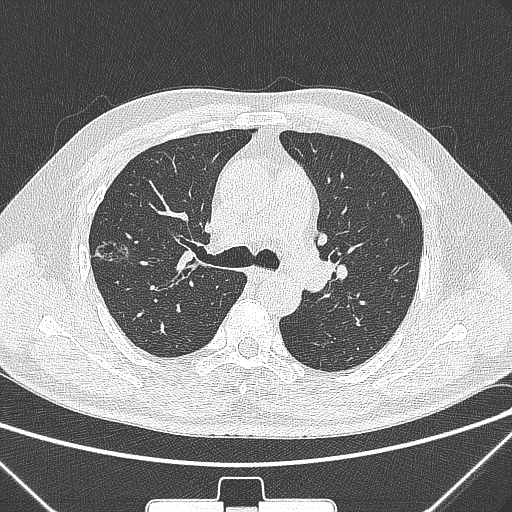
Chest CT, one axial slice; position 199 of 320 along the scan axis; 120 kVp; lung window (W 1500 / L -600 HU); 512 × 512 image matrix. Patient: male, 58 years. From the clinical record (not read from this slice): clinical TNM (as recorded): T1c N0 M0; histopathological grade: G2.
Outlined on this slice (rectangle marked by the reading radiologist):
- lung tumour (recorded histology: adenocarcinoma): box from (x=85, y=233) to (x=133, y=272) px